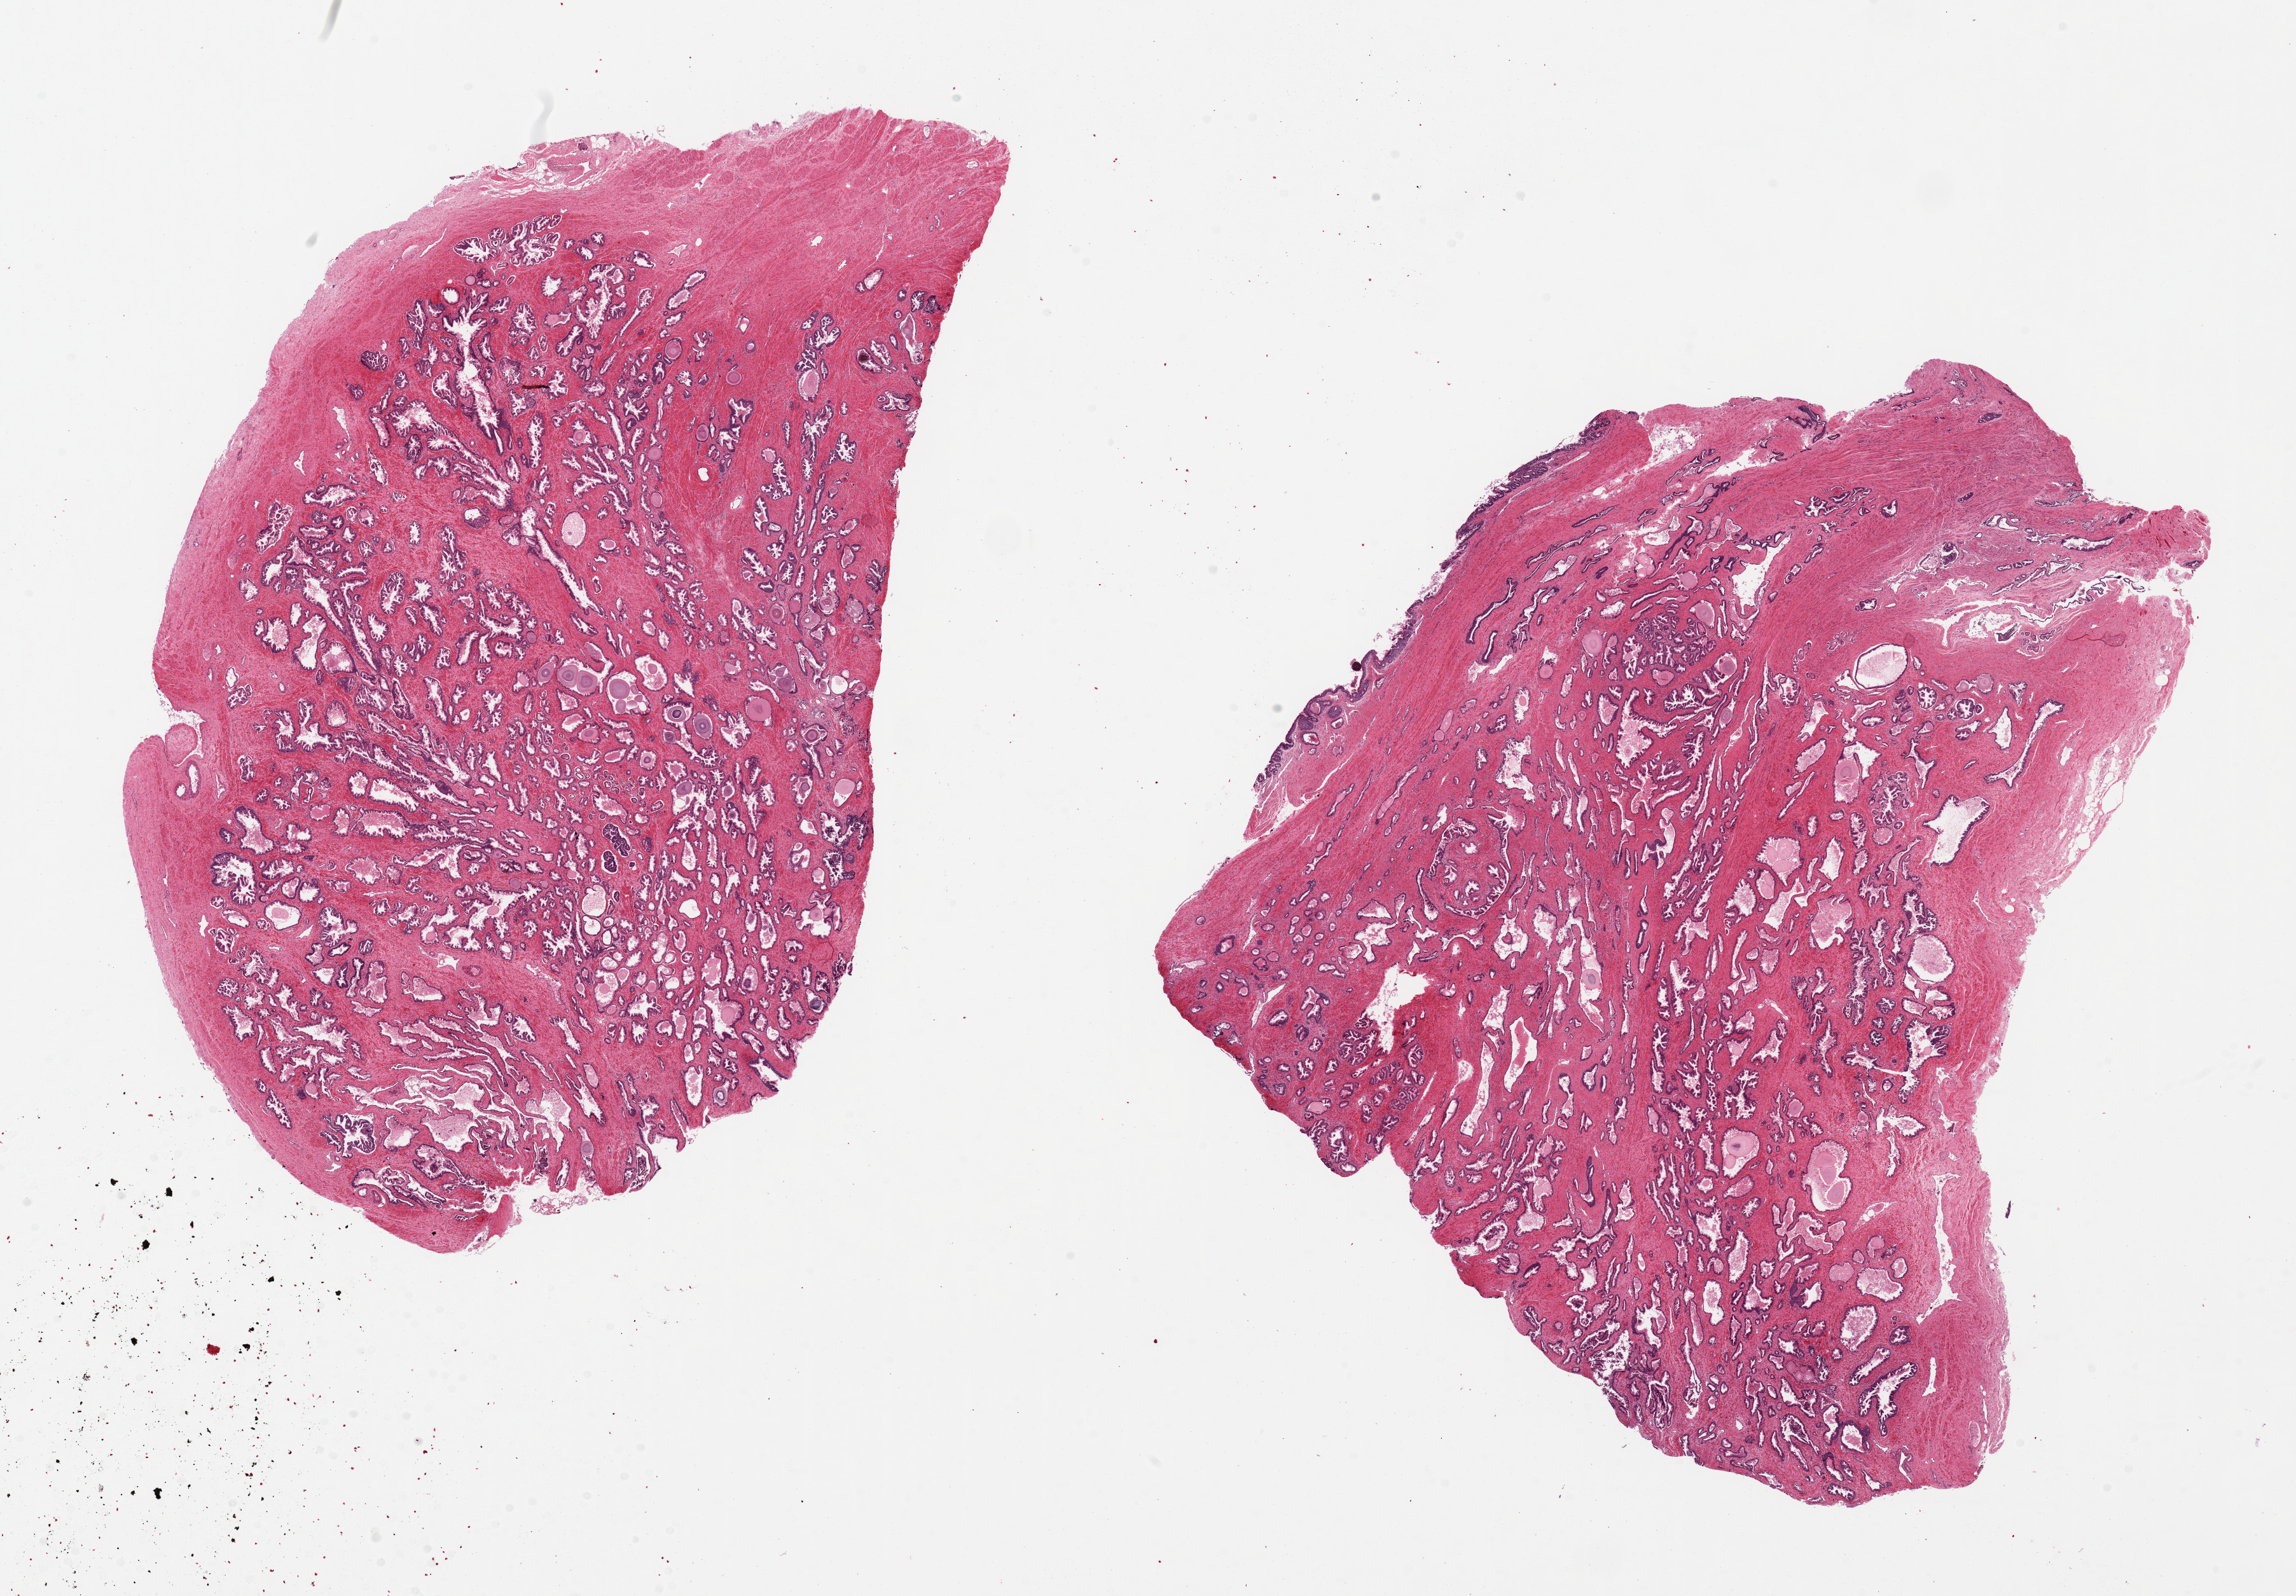
Whole-slide image, H&E stain — a low-resolution overview of the entire scanned area, about 28.5 x 19.8 mm; PAXgene-fixed, paraffin-embedded tissue; target tissue: prostate; tissue donor sample. Male donor.
Pathologist's review note for this sample: 2 pieces ~13x9mm; Well preserved glands; Thin layer of prostatic urethral epithelium along one edge.